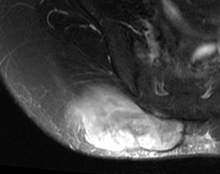
MRI of an extremity soft-tissue mass, one axial slice. Slice 38 of 63 in the series (ordered by position). T2-weighted fat-saturated. MR volume resampled by the dataset authors to the PET/CT grid (not the native acquisition matrix). 3.27 mm slice thickness. 220 × 174 image matrix. Female patient. From the clinical record (not read from this slice): histological type: spindle cell suggestive of myxofibrosarcoma; grade: intermediate; site of the primary tumour: right buttock.
Outlined on this slice (expert contour drawn on MRI and transferred to this co-registered scan by the dataset authors):
- gross tumour volume (mass): bounding box [x1, y1, x2, y2] px = [68, 91, 183, 153]